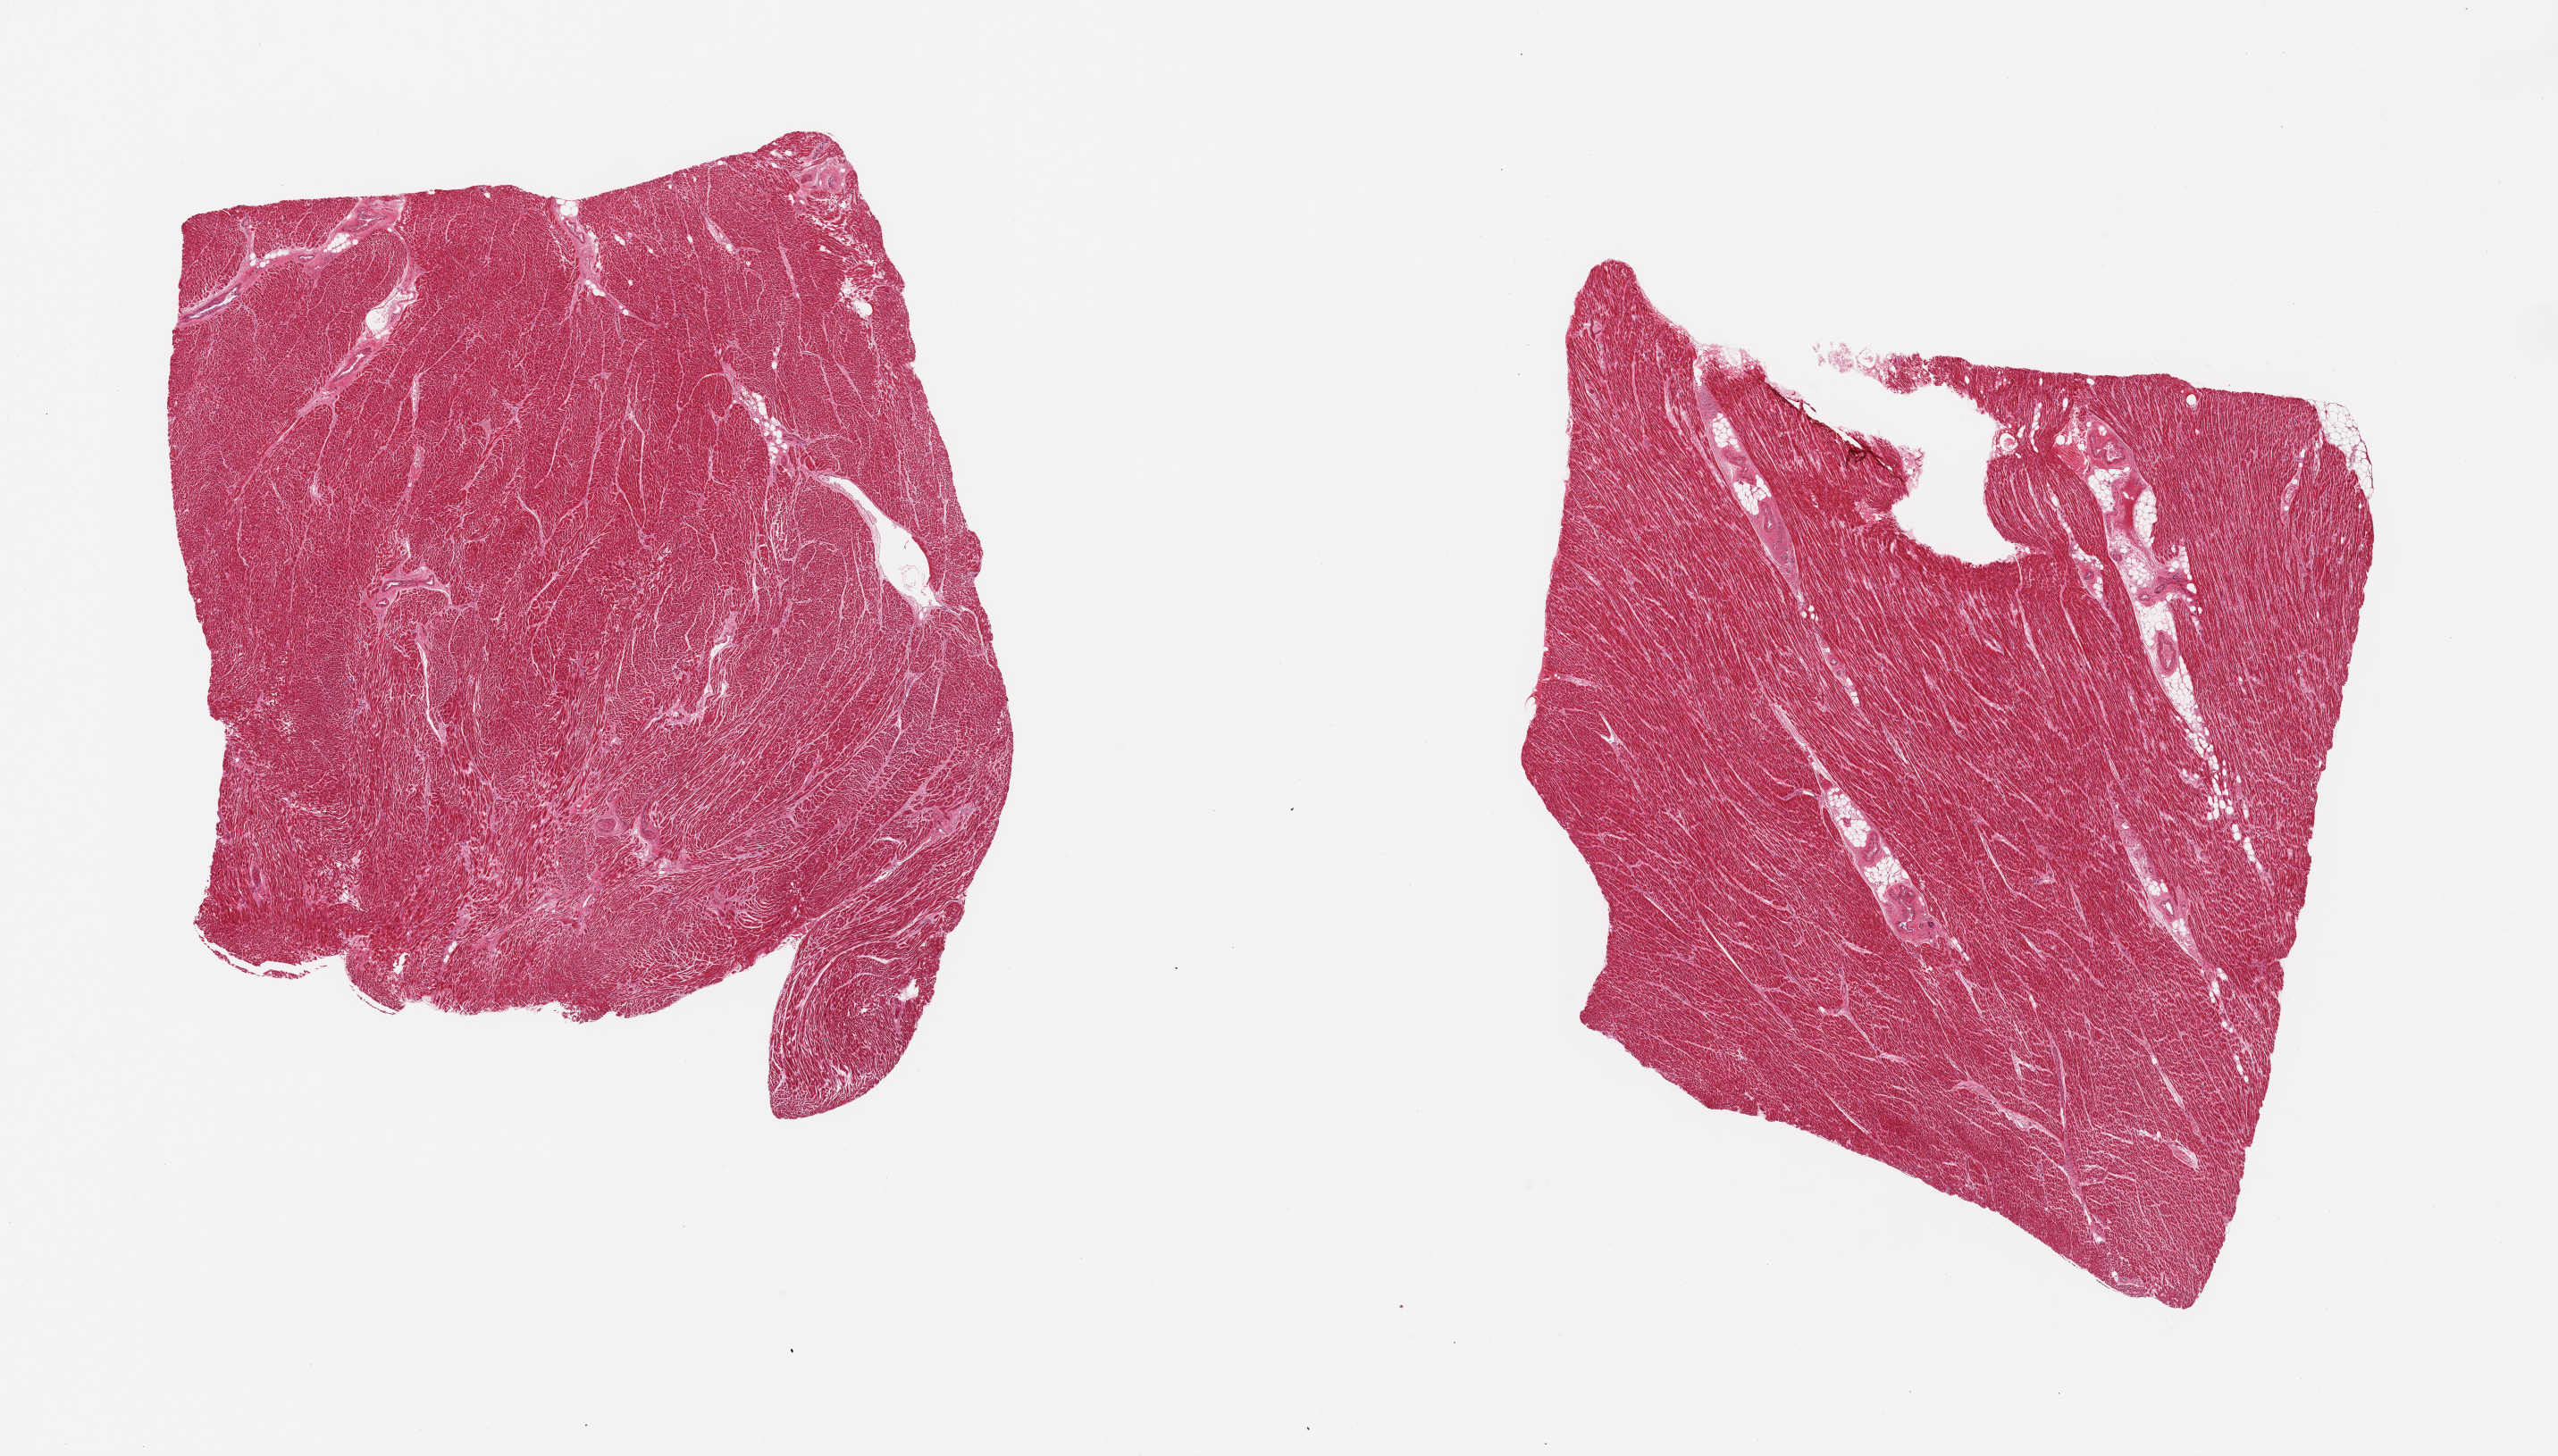
Digitized H&E-stained section, brightfield — shown as a low-resolution overview of the whole scanned area (about 22.6 x 12.9 mm, slide scanned at 20x); PAXgene-fixed paraffin-embedded (PFPE) section; target tissue: heart; tissue donor sample. Female donor.
• reviewer comment on this tissue sample: 2 pieces; <5% internal fat